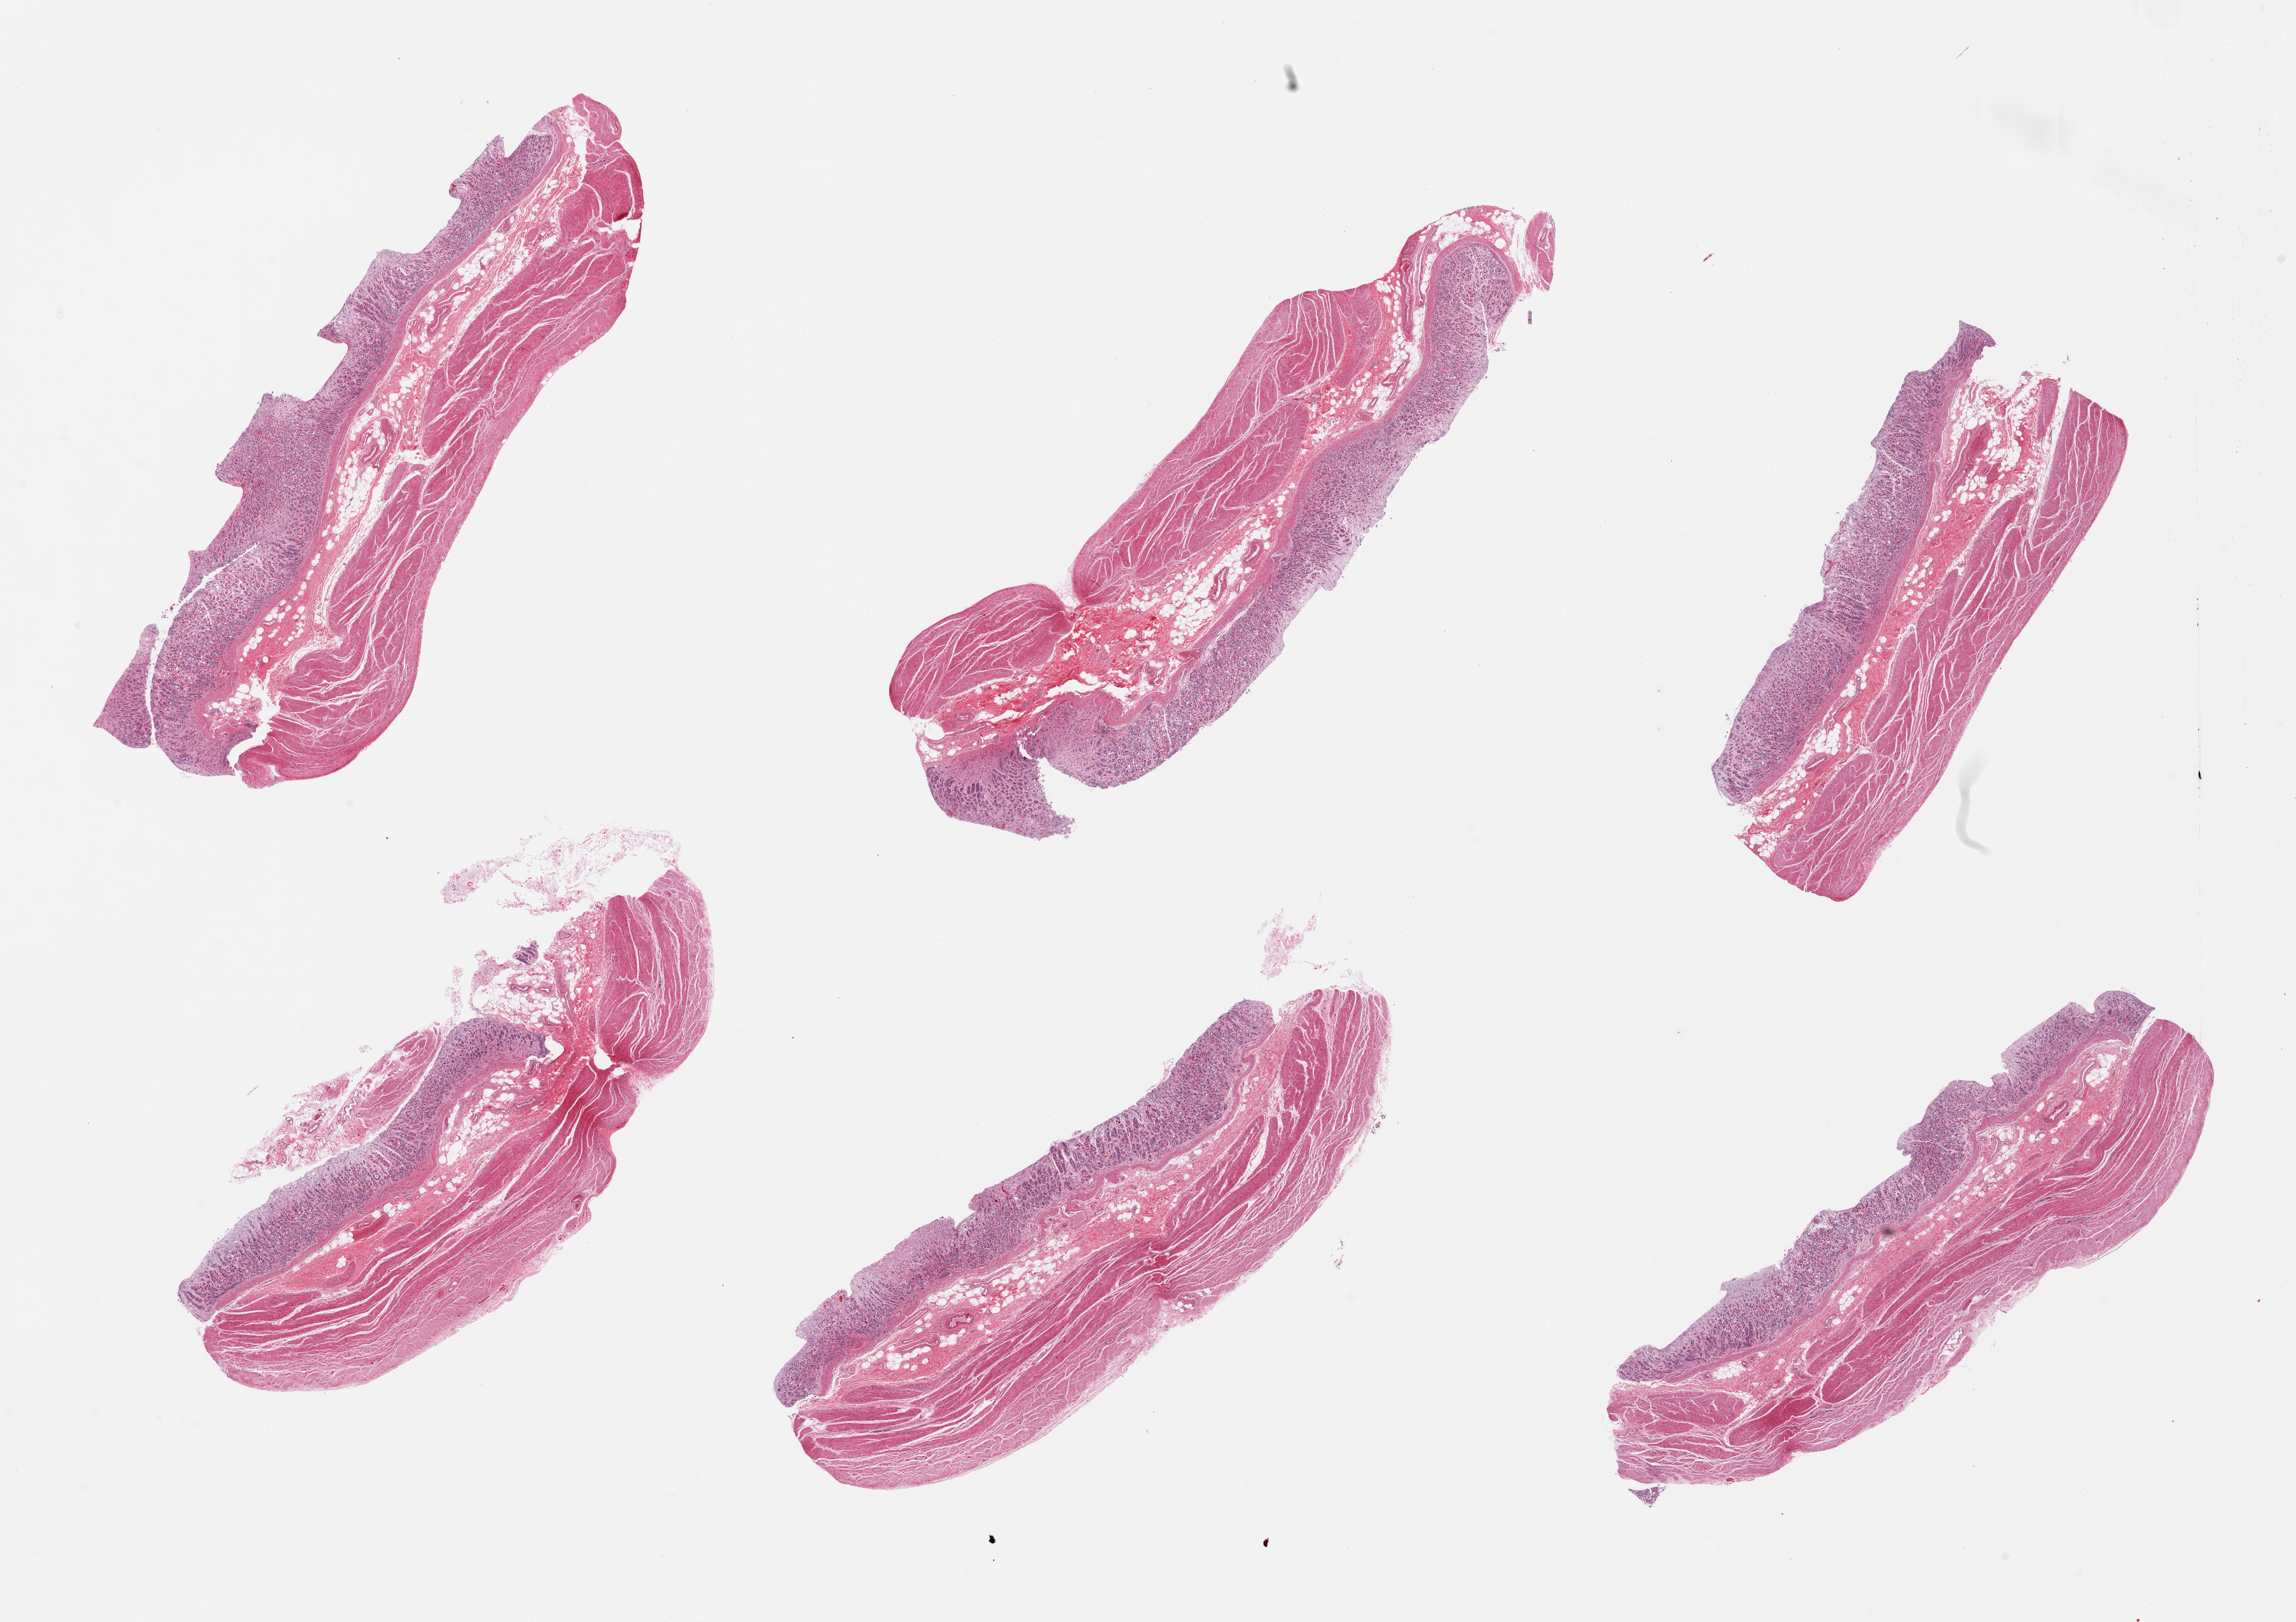
Whole-slide image, haematoxylin and eosin stain, shown as a low-resolution overview of the whole scanned area (about 28.5 x 20.2 mm). PAXgene-fixed, paraffin-embedded tissue. Sampled site (target tissue): stomach. Donor tissue sample. Donor sex: male.
Reviewer comment on this tissue sample: 6 pieces; full thickness well dissected.